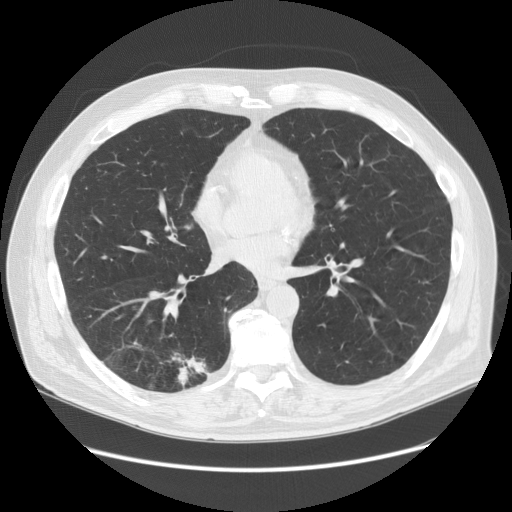
Low-dose screening chest CT, one axial slice; position 66 of 149 along the scan axis; 120 kVp; lung window (W 1500 / L -600 HU); 2.5 mm slice thickness; 512 × 512 image matrix.
Annotated regions visible in this slice (manually delineated by an expert):
- lesion 1 (tumor, lower lobe of right lung): bounding box (x1, y1, x2, y2) in pixels: (172, 353, 207, 387)